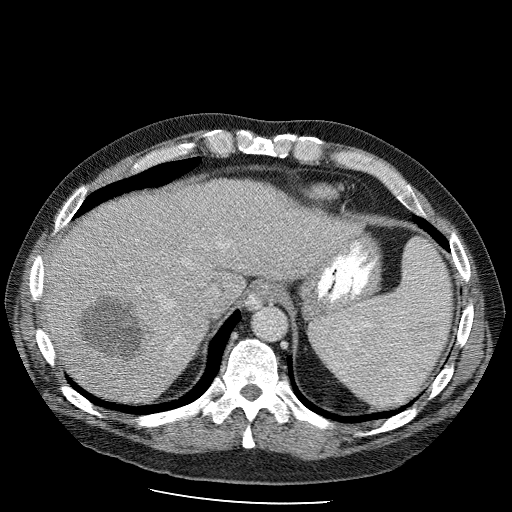
Contrast-enhanced abdominal CT (liver protocol), one axial slice. Soft-tissue window (W 400 / L 40 HU). 2.5 mm slice thickness. 512 × 512 image matrix, field of view 400 × 400 mm. From the clinical record (not read from this slice): diagnosis: hepatocellular carcinoma (patient treated with transarterial chemoembolisation; whether this scan precedes or follows treatment is not stated here); TNM stage (as recorded): Stage-II; Child-Pugh class: B.
Outlined on this slice (semi-automatic segmentation, software-assisted and operator-edited):
- liver parenchyma outside the tumour (the mass and vessels are separate outlines, so this box may not span the whole liver): bounding box (x1, y1, x2, y2) in pixels: (39, 180, 358, 398)
- mass: (75, 292, 153, 365)
- liver vessels: (197, 292, 207, 305)